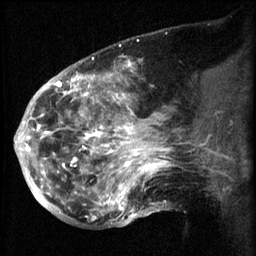
Breast MRI (dynamic contrast-enhanced), one sagittal slice. Slice 26 of 60 in the series (ordered by position). 3 images stored at this slice position (order not interpretable as contrast timing). 1.5 T. TE 4.2 ms, TR 8.2 ms. 256 × 256 image matrix, field of view 200 × 200 mm. Patient: female, 50 years.
Annotated regions visible in this slice (semi-automatic segmentation, software-assisted and operator-edited):
- analysis volume of interest (the breast-tissue region the enhancement analysis was run in; not a lesion): bounding box (x1, y1, x2, y2) in pixels: (50, 64, 169, 217)
- tumour enhancement mask (voxels above the 70 % enhancement threshold inside the analysis volume of interest): (50, 64, 169, 217)